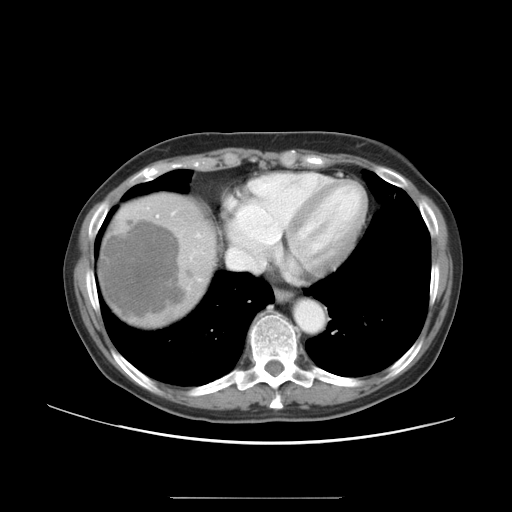
Contrast-enhanced abdominal CT, one axial slice. Slice 43 of 50 in the series (ordered by position). 120 kVp. Intravenous contrast given. Soft-tissue window (W 400 / L 40 HU). 5 mm slice thickness. 512 × 512 image matrix, field of view 389 × 389 mm. Female patient, age 58 years. Case-level facts recorded for this patient, not image findings: diagnosis: colorectal cancer liver metastases, imaged before liver resection; multiple liver metastases: yes; largest metastasis: 7.3 cm; disease in both lobes: yes.
Annotated regions visible in this slice (outlined manually by an expert reader):
- hepatic veins: bounding box [x1, y1, x2, y2] px = [226, 239, 267, 271]
- liver: [100, 198, 214, 325]
- portal vein (with intrahepatic branches): [156, 215, 159, 218]
- liver metastasis: [100, 218, 187, 320]